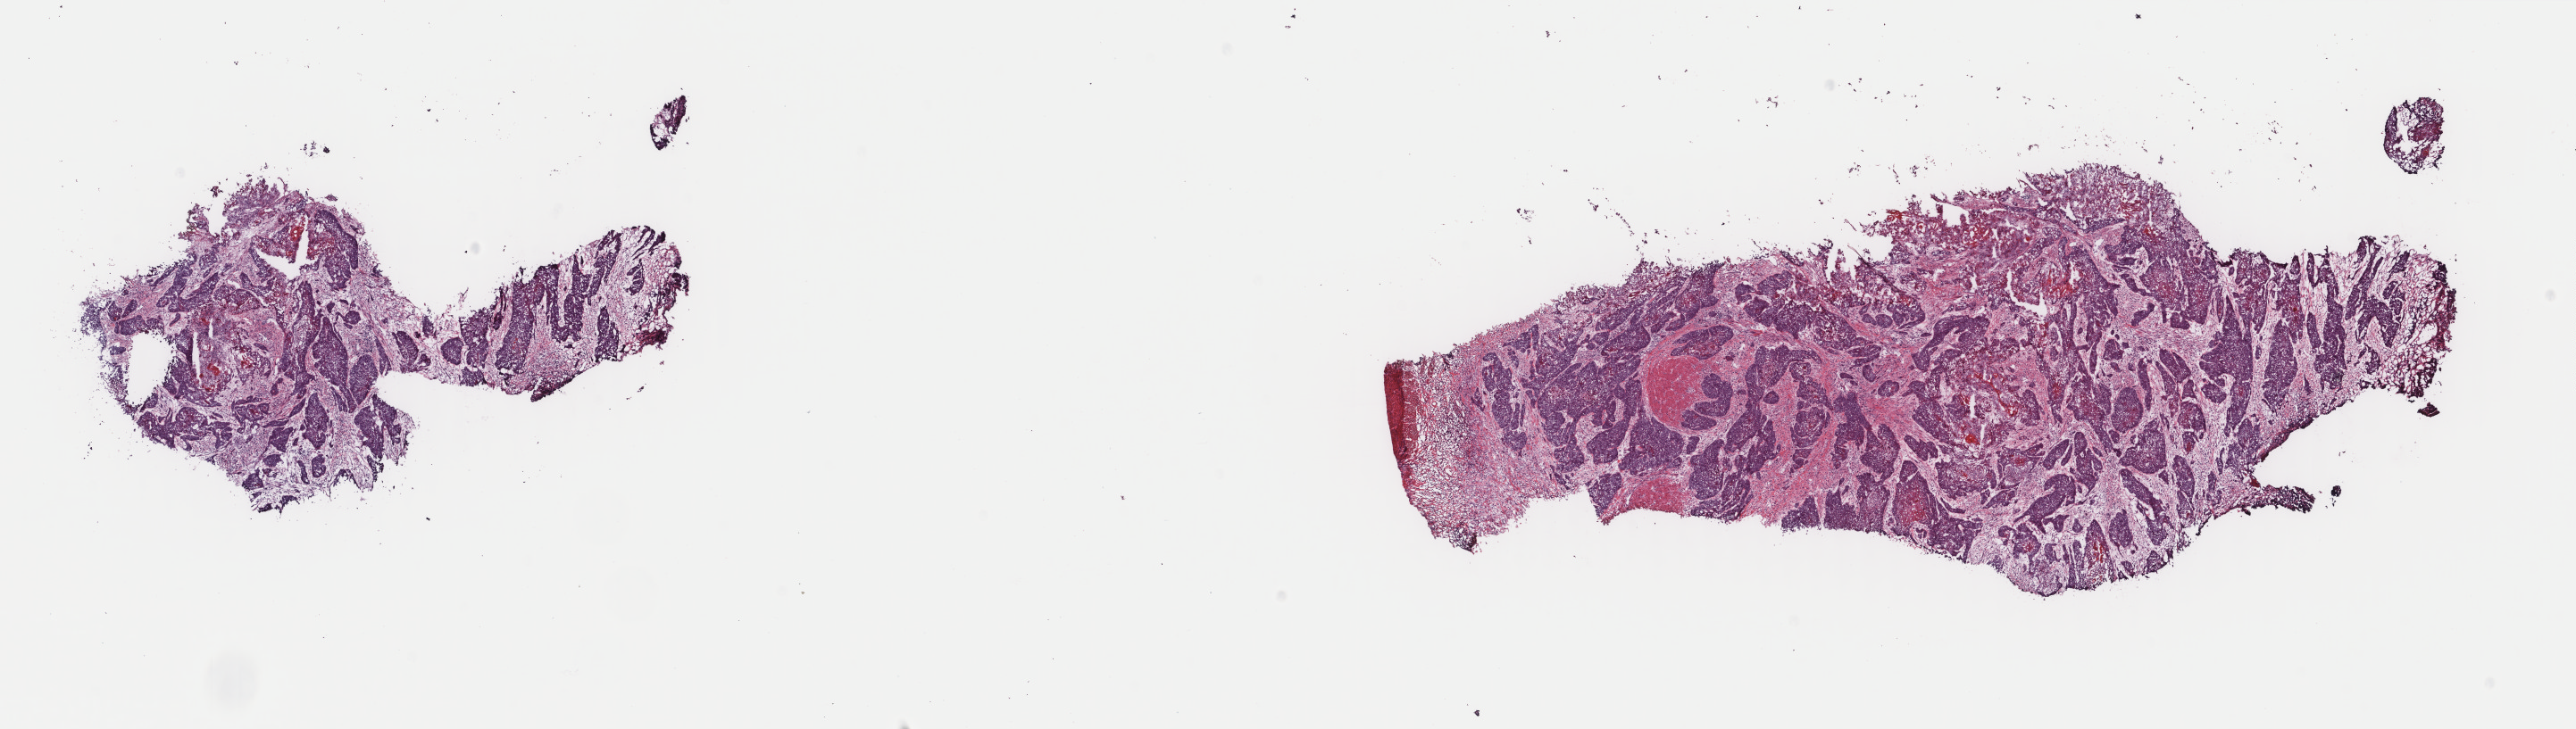
Digitized H&E tissue section (whole slide) — whole scanned area (about 22.9 x 6.5 mm, acquisition: 40x scan) shown as a low-resolution overview; frozen section from the top of the tissue portion; primary tumour sample from the bladder. Male patient; age at initial diagnosis 67 years. Histologic grade: high grade. Slide review estimates, as recorded: tumour cells 70%, tumour nuclei 70%, normal cells 0%, stromal cells 27%, necrosis 3%. Infiltration values recorded for this section: lymphocyte infiltration 7%, monocyte infiltration 1%, neutrophil infiltration 3%.
- diagnosis: Transitional cell carcinoma
- AJCC pathologic stage: III (7th edition)
- lymph nodes positive (case pathology): 0 of 68 examined